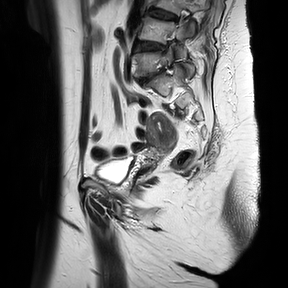
Pelvic MRI for cervical cancer, one sagittal slice. Position 24 of 37 along the scan axis. T2-weighted. 1.5 T. TE 100 ms, TR 4174.1 ms. 288 × 288 image matrix, field of view 300 × 300 mm. Female patient, age 65 years.
Annotated regions visible in this slice (outlined manually by an expert reader):
- uterus and cervix: bounding box [x1, y1, x2, y2] px = [142, 111, 177, 169]